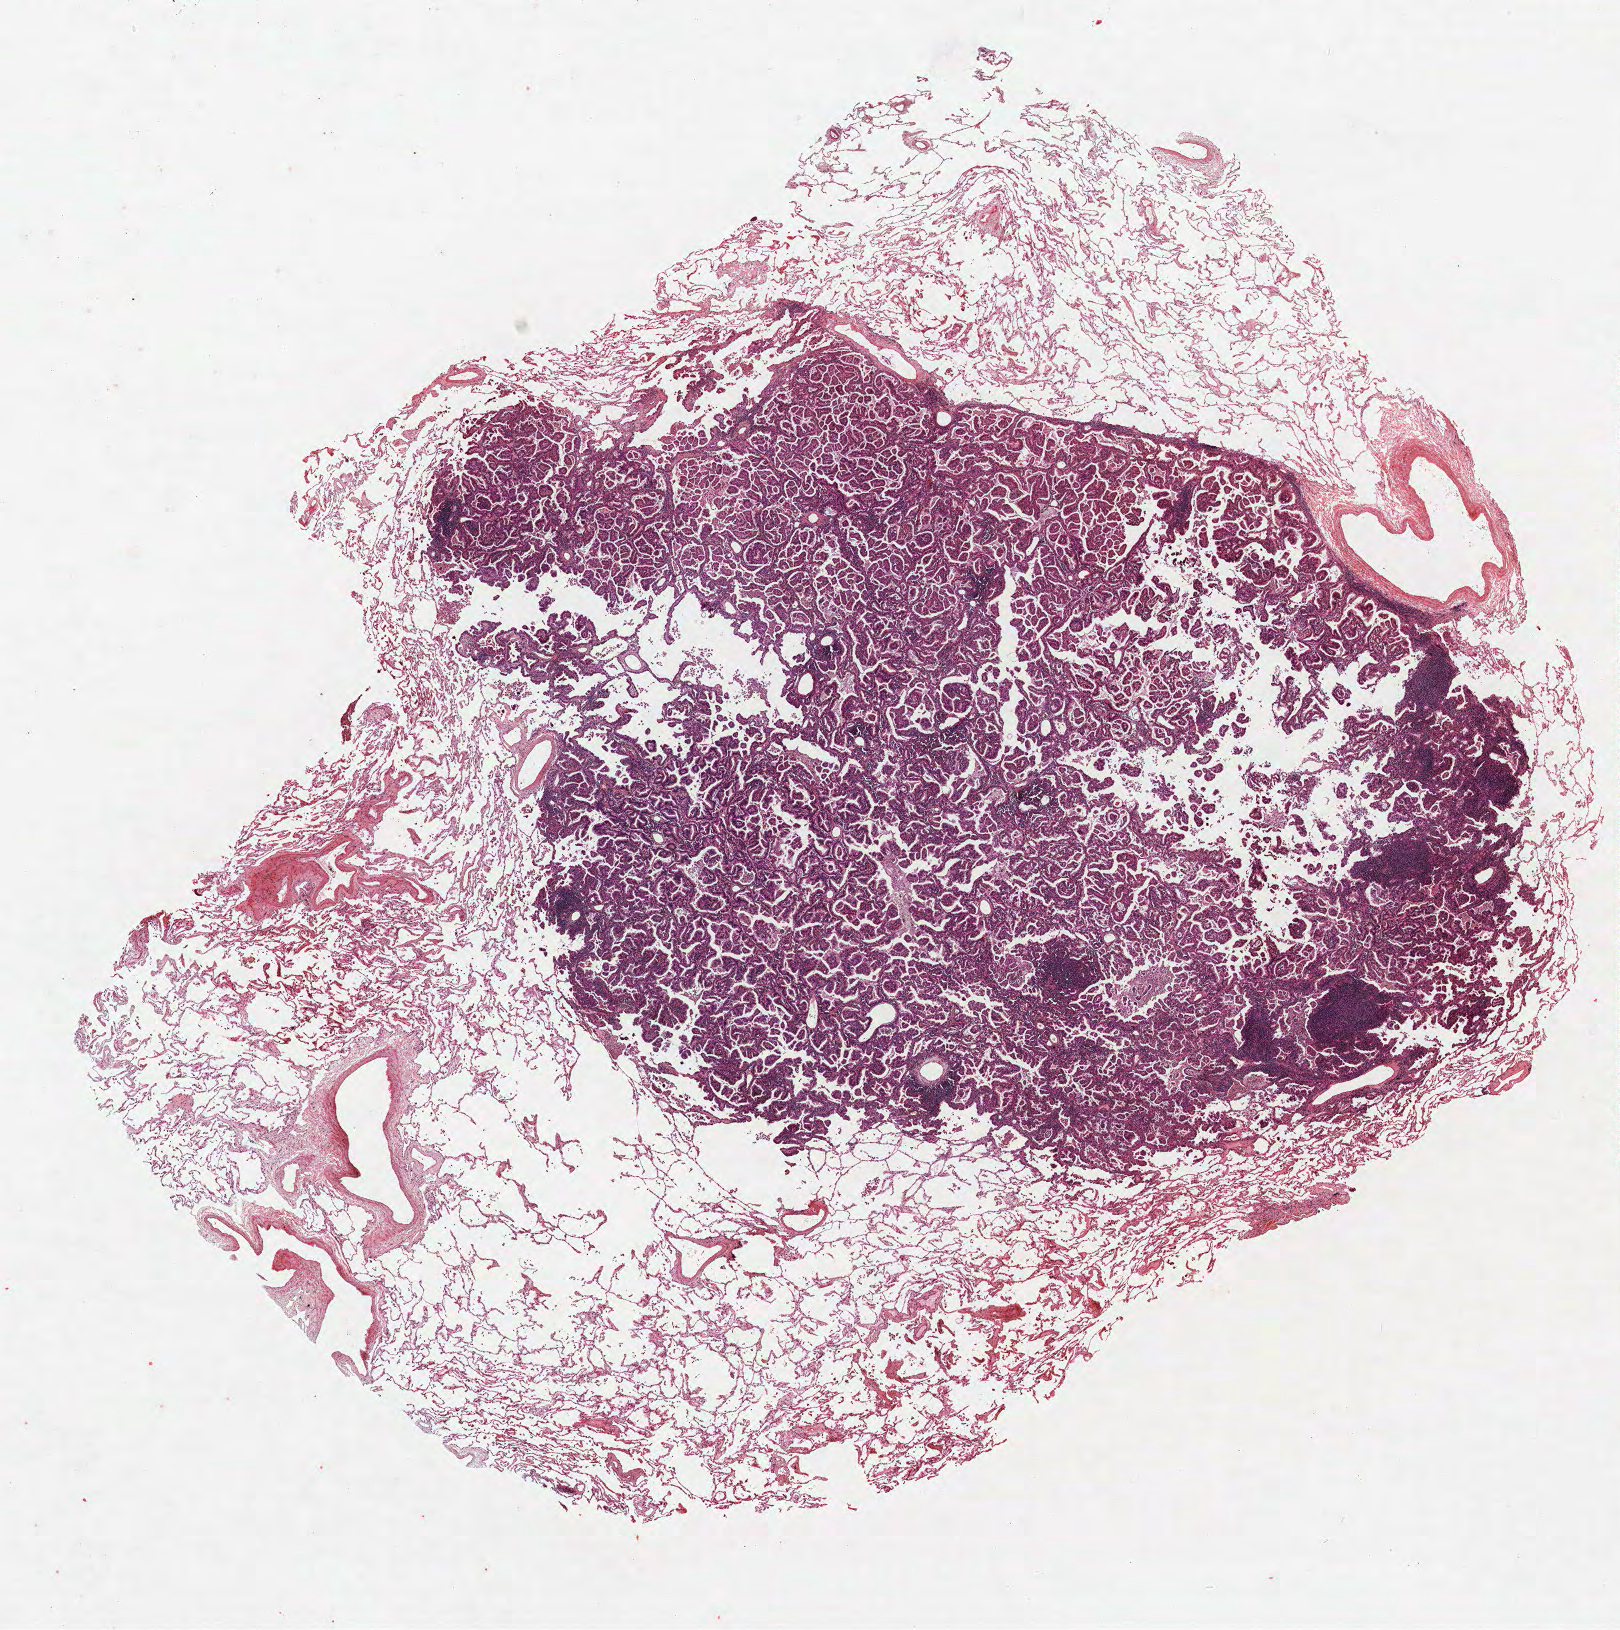
Whole-slide histology image, H&E — shown as a low-resolution overview of the whole scanned area (about 13.0 x 13.0 mm, slide scanned at 40x), FFPE section, lung tissue. Female, age 66 at enrolment.
Participant's lung-cancer diagnosis: Bronchiolo-alveolar carcinoma, mucinous.